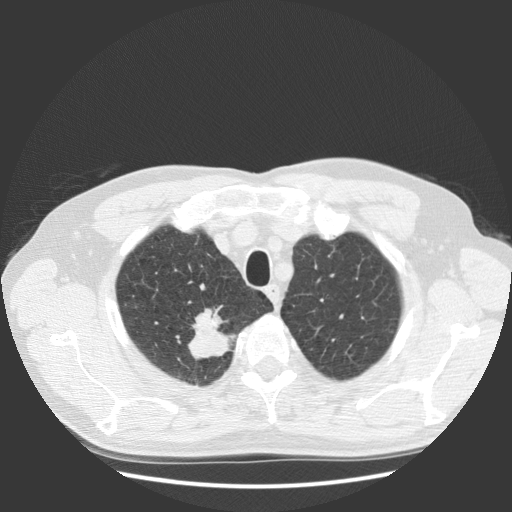
Low-dose screening chest CT, one axial slice; position 108 of 131 along the scan axis; reconstruction kernel STANDARD; 140 kVp; lung window (W 1500 / L -600 HU); 512 × 512 image matrix, field of view 369 × 369 mm.
Structures marked on this image (manually delineated by an expert):
- lesion 1 (tumor, upper lobe of right lung): bounding box [x1, y1, x2, y2] px = [188, 308, 235, 360]